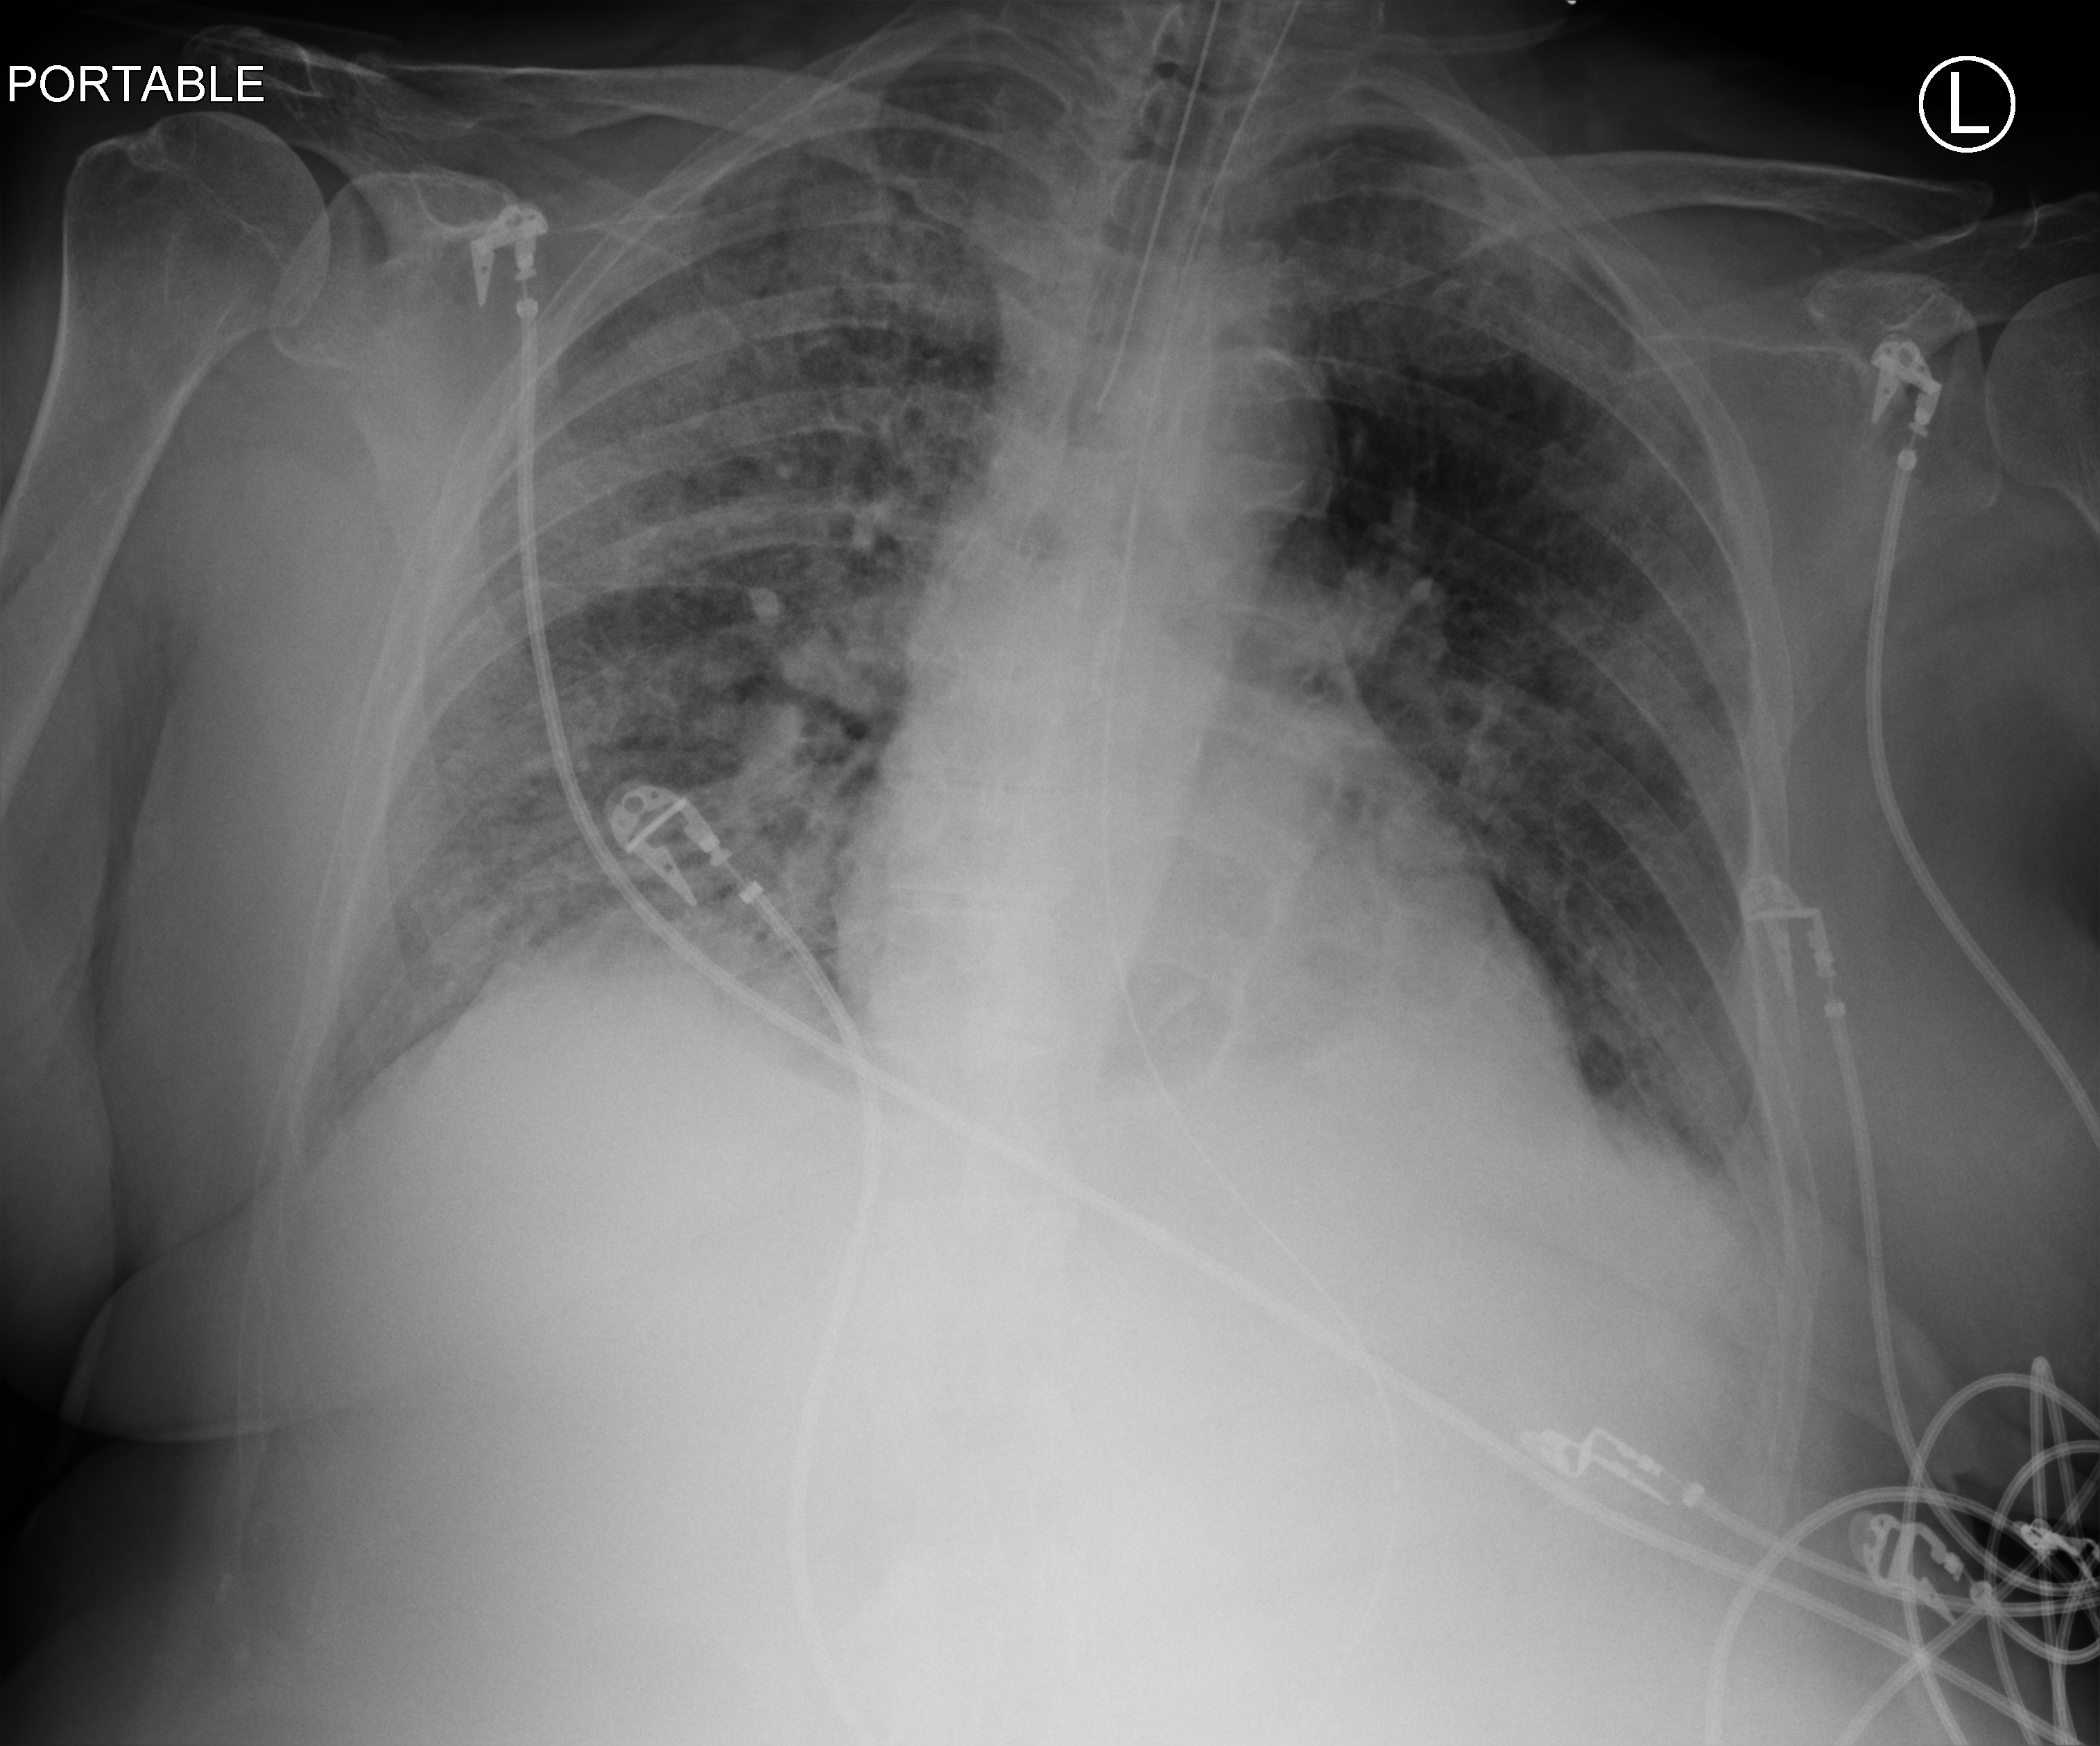
Chest X-ray (portable). Patient hospitalised with COVID-19; female, aged 75–90 years.
Admission-level facts for this patient (not findings on this image; timing relative to this image not recorded): mechanically ventilated during this hospital stay: yes.